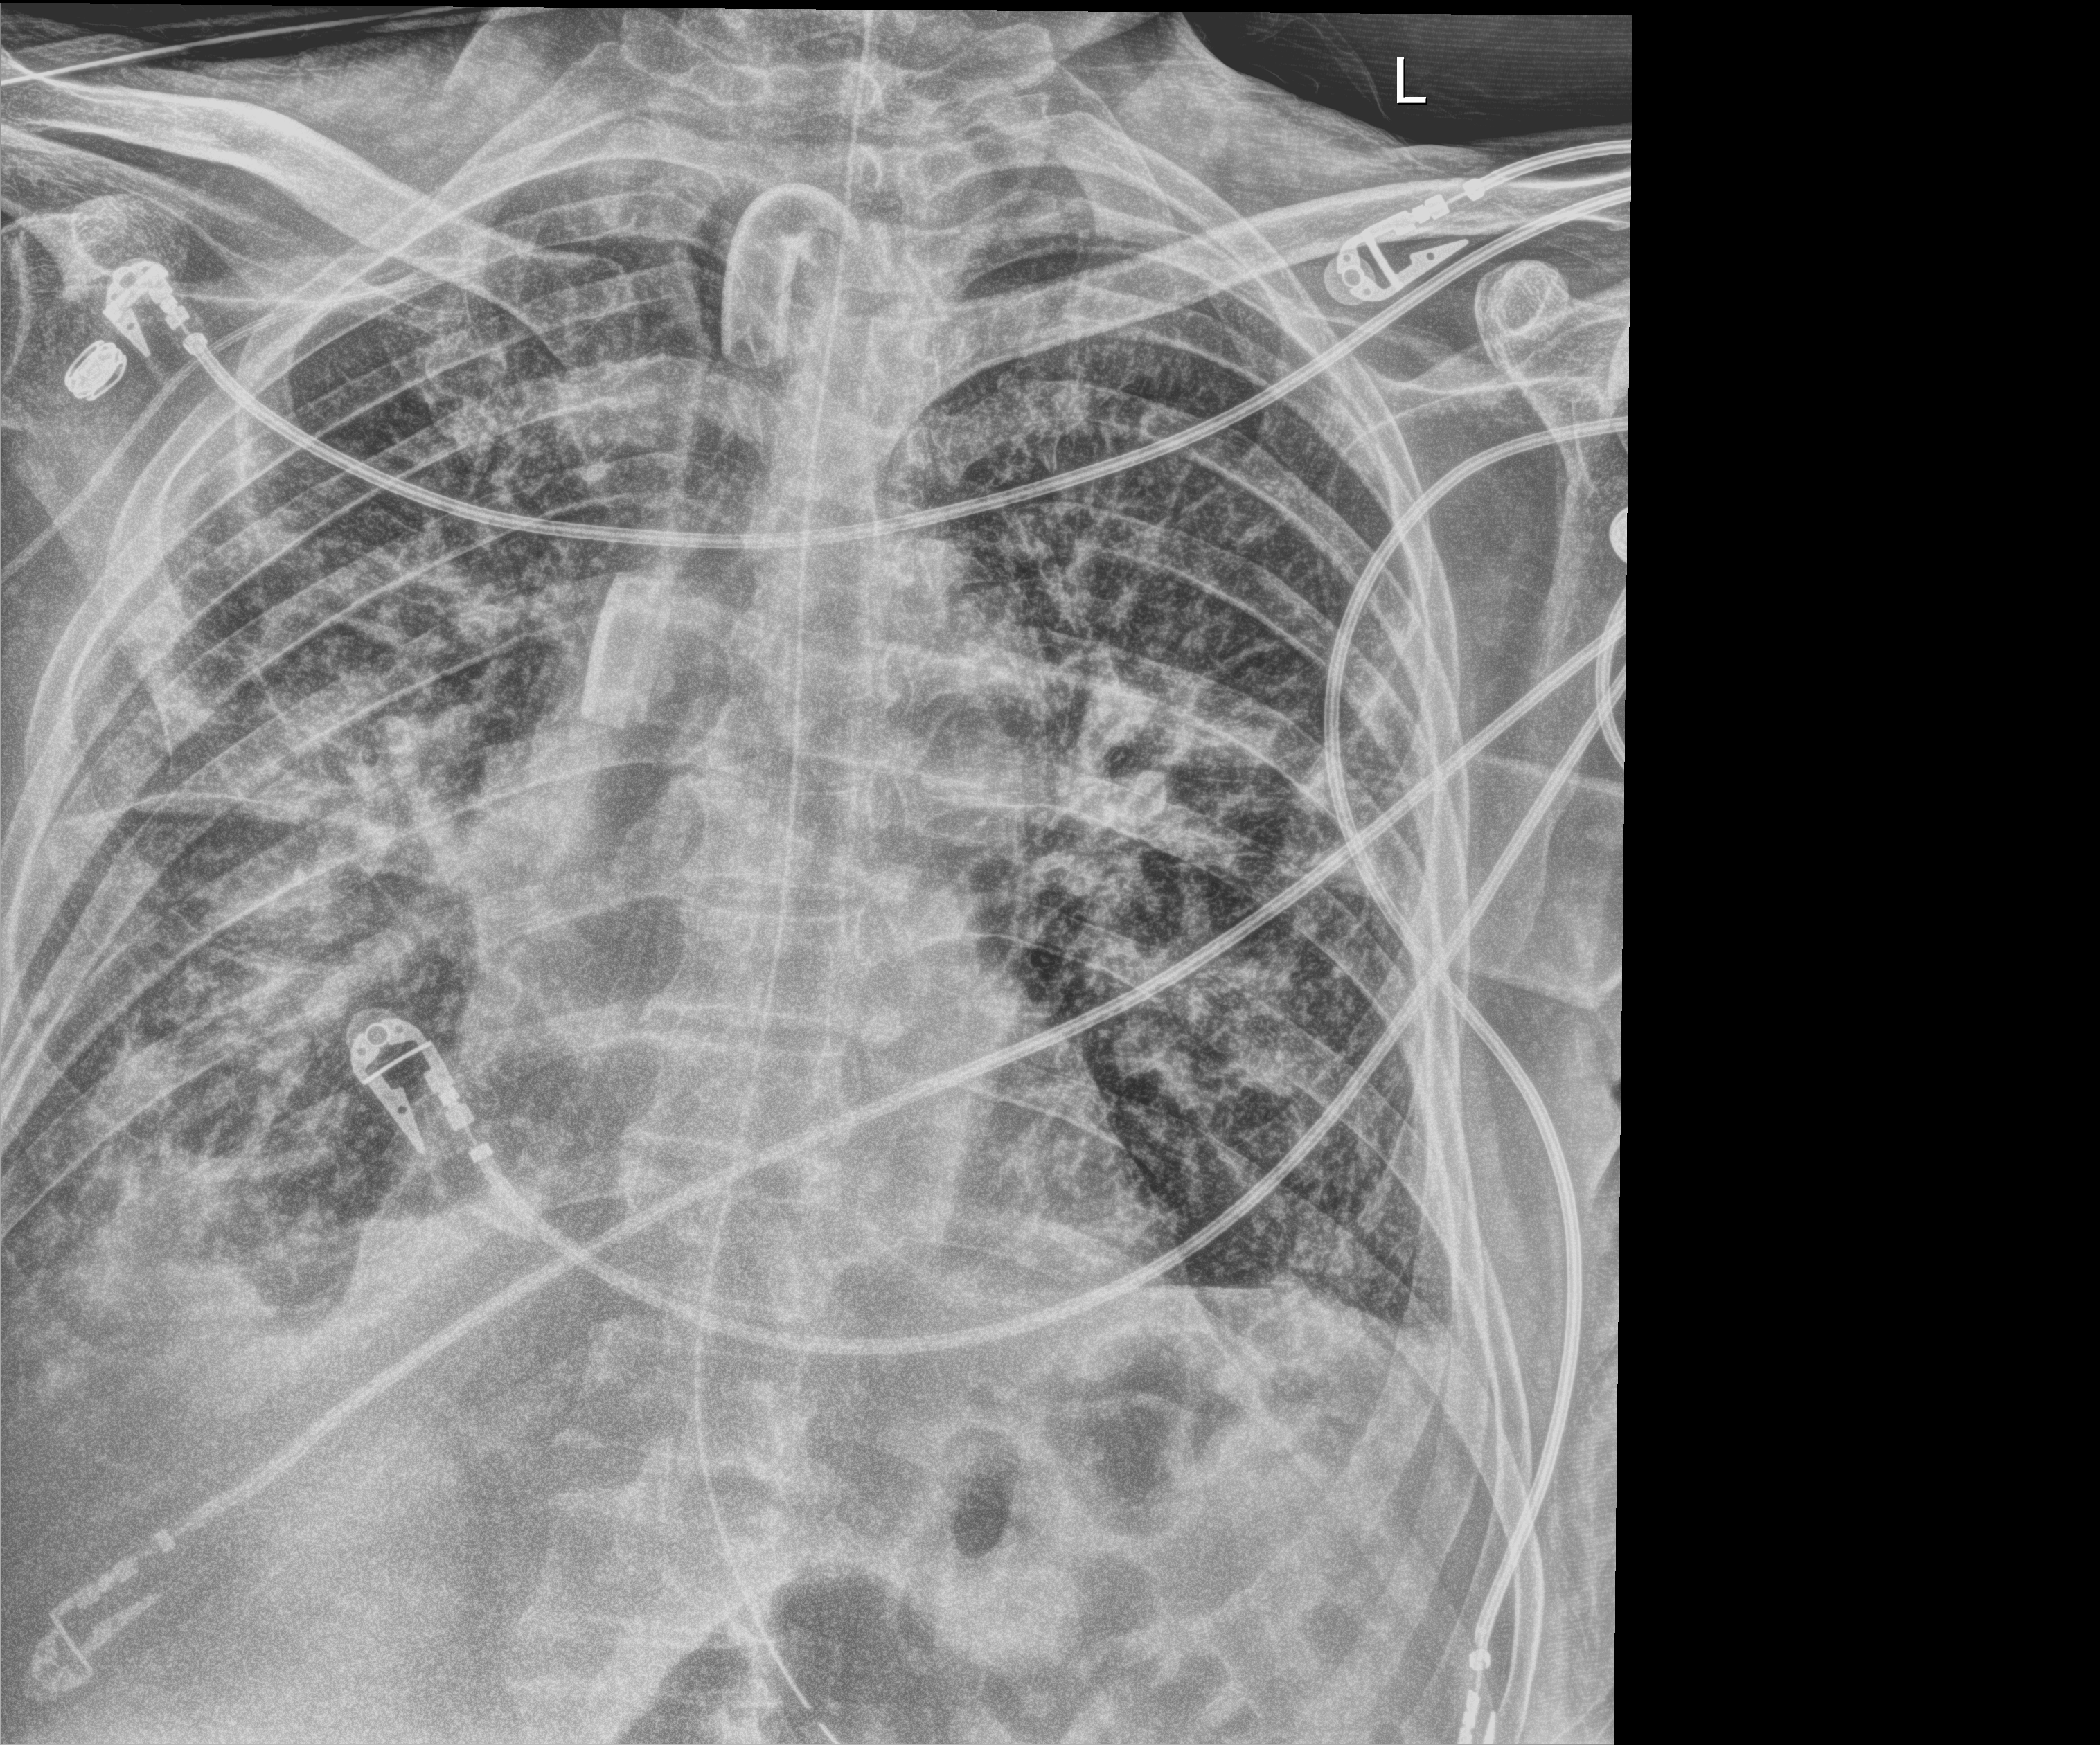
Bedside chest radiograph (digital radiography), anteroposterior (AP) projection. Patient hospitalised with COVID-19; male, aged 75–90 years.
Admission-level facts for this patient (not findings on this image; timing relative to this image not recorded):
- admitted to intensive care during this hospital stay: yes
- length of hospital stay: 70 days
- mechanically ventilated during this hospital stay: yes